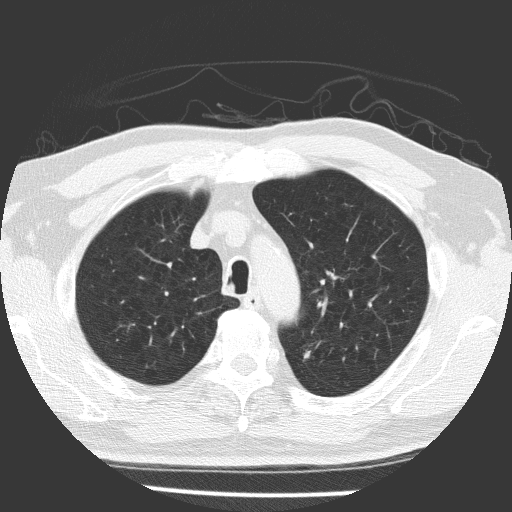
Low-dose screening chest CT, one axial slice. Position 131 of 169 along the scan axis. Reconstruction kernel FC51. 120 kVp. Lung window (W 1500 / L -600 HU). 512 × 512 image matrix.
Annotated regions visible in this slice (outlined manually by an expert reader):
- lesion 1 (tumor, upper lobe of left lung): bounding box (x1, y1, x2, y2) in pixels: (304, 351, 311, 359)